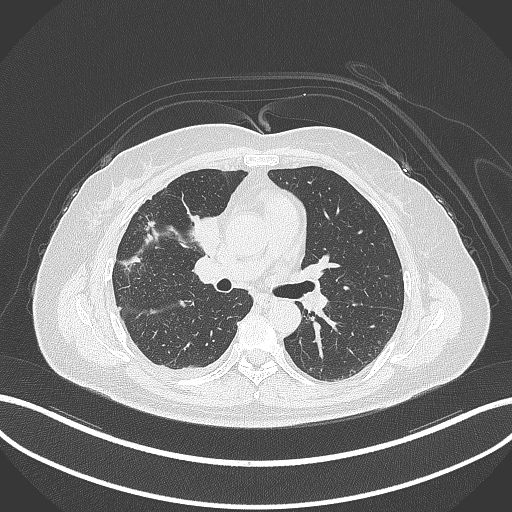
Chest CT, one axial slice. Position 156 of 305 along the scan axis. Lung window (W 1500 / L -600 HU). 1 mm slice thickness. 512 × 512 image matrix. Patient: female, 52 years. Case-level facts recorded for this patient, not image findings: clinical TNM (as recorded): T3 N1 M1.
Annotated regions visible in this slice (rectangle marked by the reading radiologist):
- lung tumour (recorded histology: adenocarcinoma): bounding box <183,205,224,259> (left, top, right, bottom; pixels)